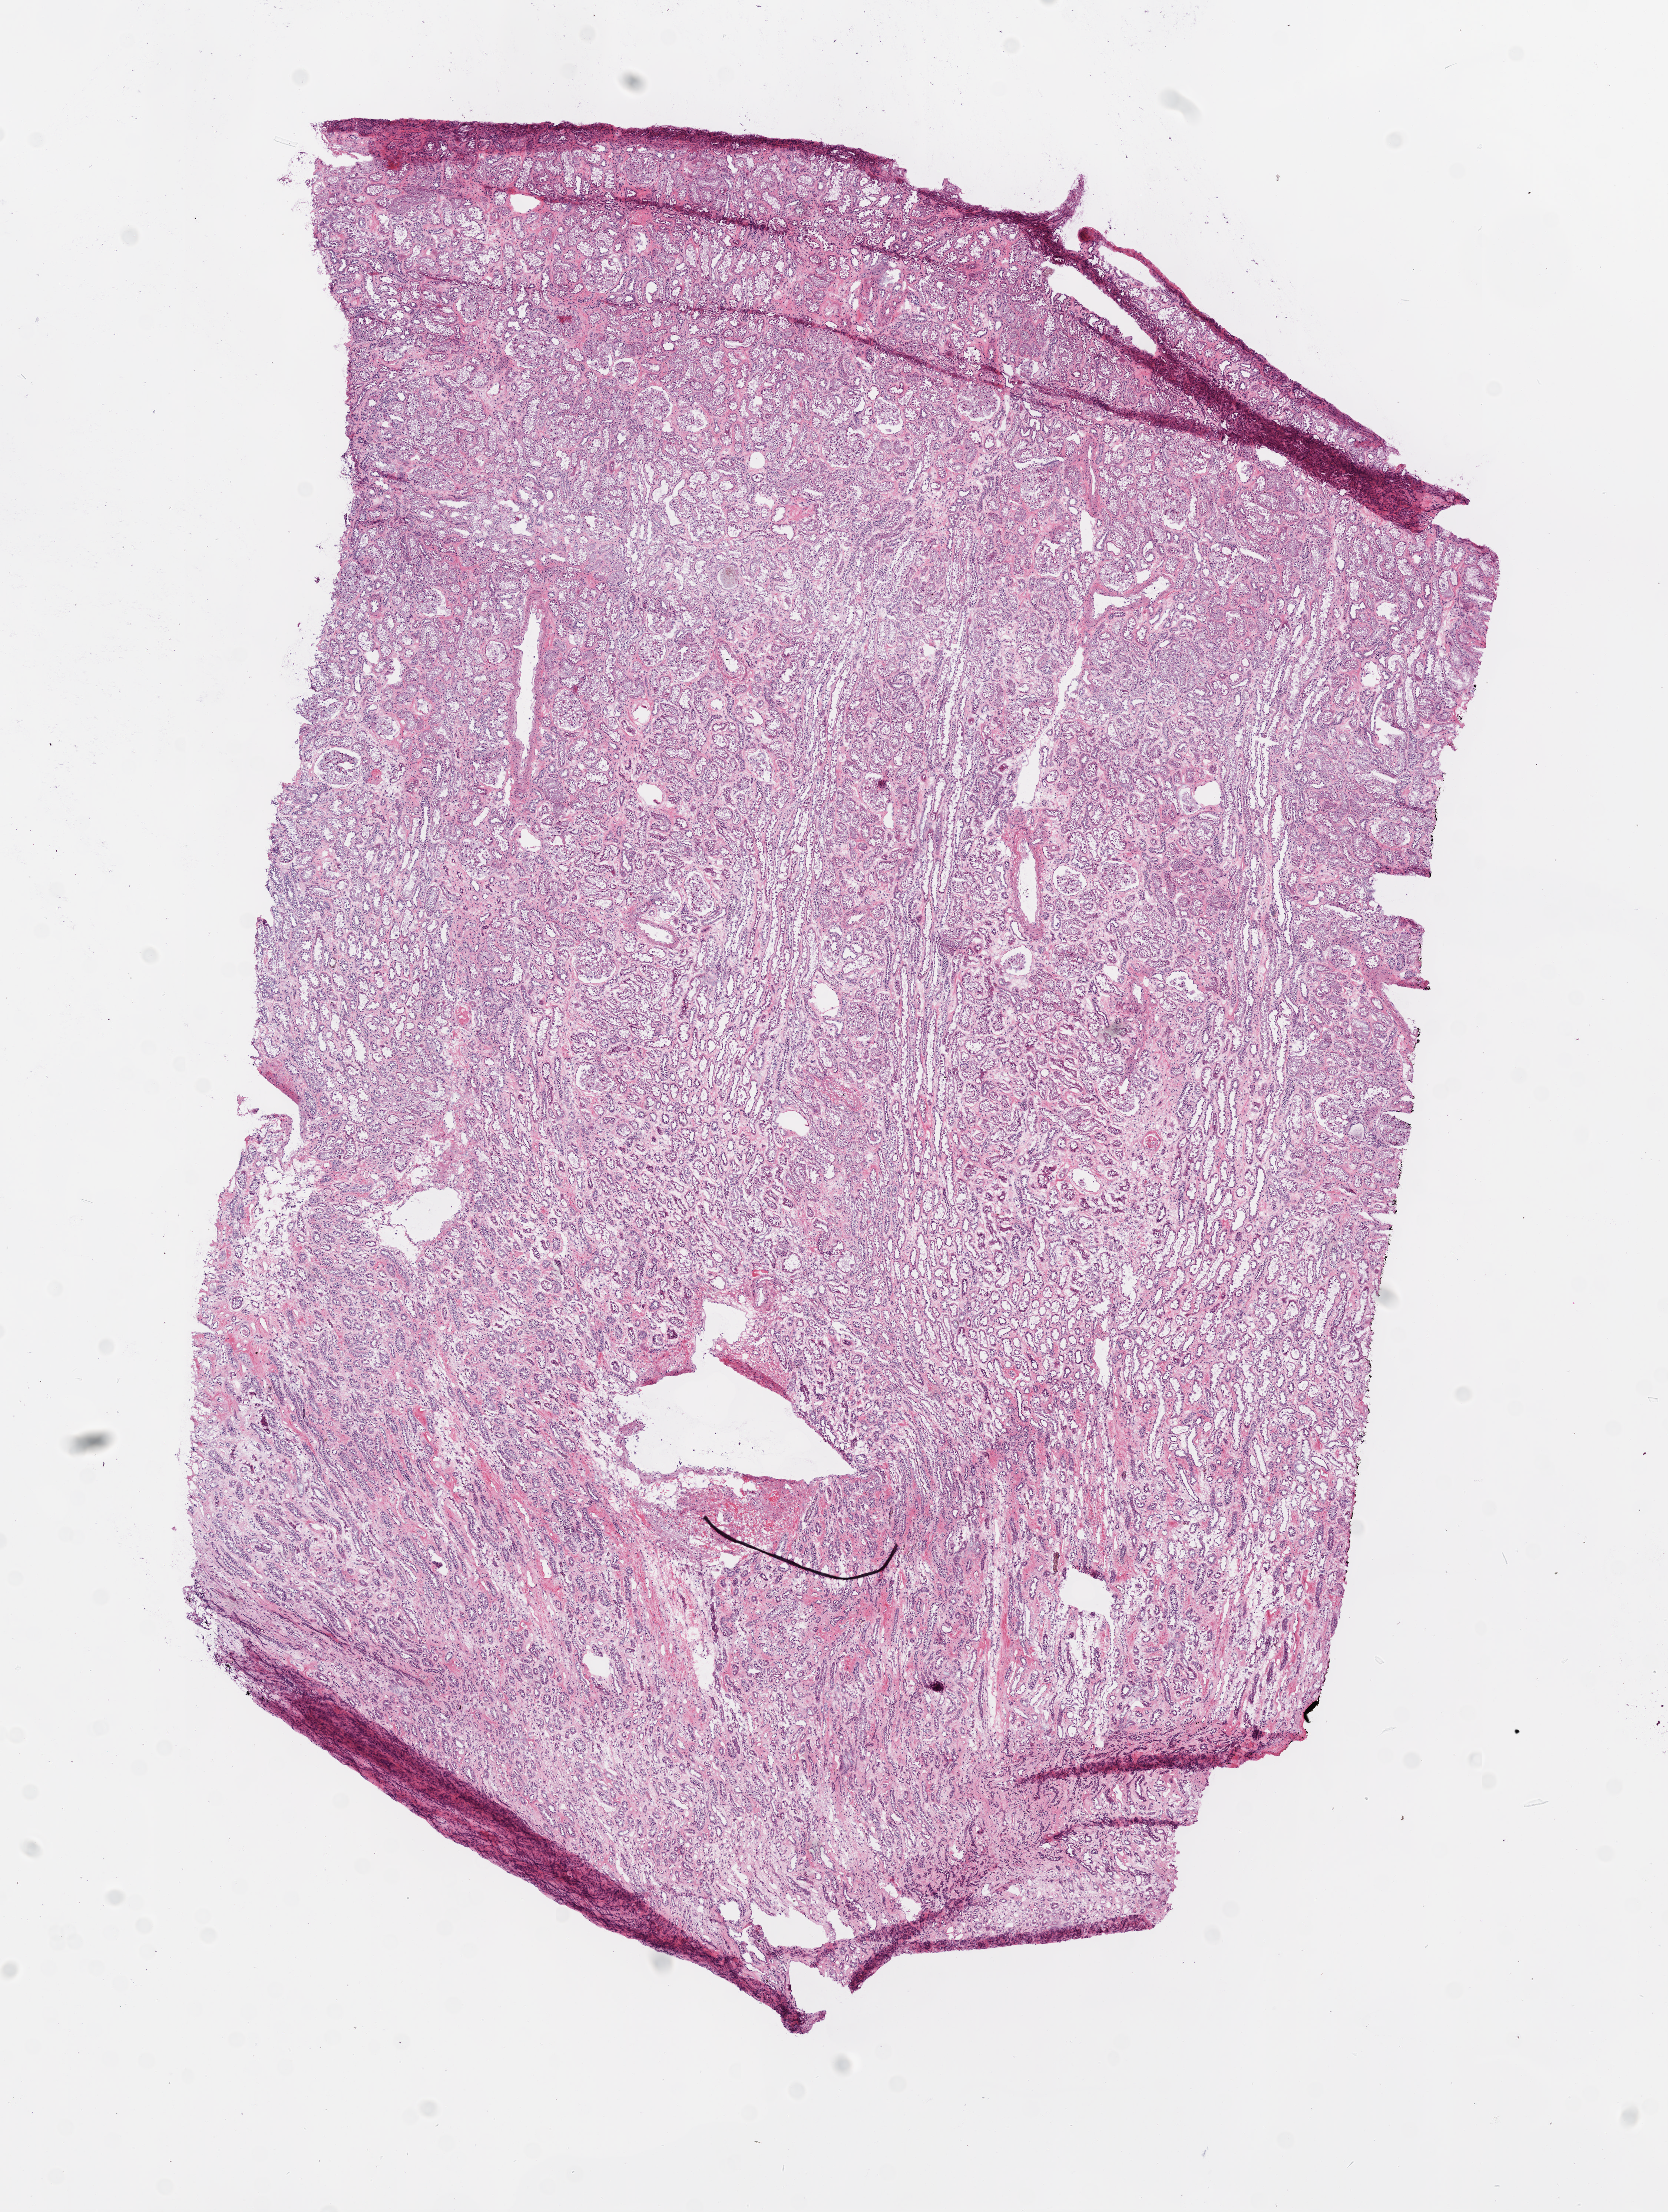
Digitized Hematoxylin and eosin (H&E) stained tissue section (whole slide), low-resolution overview of the scanned area, about 9.0 x 12.0 mm (slide scanned at 20x); frozen section from the top of the tissue portion; kidney, solid tissue normal (non-tumour tissue) sample. Male, age 67 years at initial diagnosis.
• this section: solid tissue normal sample (biorepository sample class)
• patient diagnosis: Clear cell adenocarcinoma, NOS